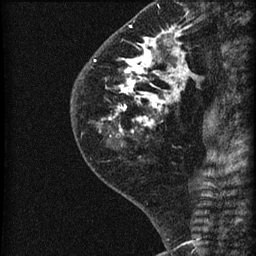
Breast MRI (dynamic contrast-enhanced), one sagittal slice. Position 23 of 60 along the scan axis. Dynamic contrast-enhanced series, image 2 of 3 at this slice position (ordered by acquisition). 1.5 T. TE 4.2 ms, TR 22.7 ms. 1.8 mm slice thickness. 256 × 256 image matrix, field of view 180 × 180 mm. Patient: female, 45 years. From the clinical record (not read from this slice): setting: breast cancer imaged before/during neoadjuvant chemotherapy; receptor status: HR-positive, HER2-negative.
Structures marked on this image (semi-automatically segmented with operator editing):
- analysis volume of interest (the breast-tissue region the enhancement analysis was run in; not a lesion): bounding box [x1, y1, x2, y2] px = [74, 11, 205, 140]
- tumour enhancement mask (voxels above the 90 % enhancement threshold inside the analysis volume of interest): [109, 28, 187, 132]